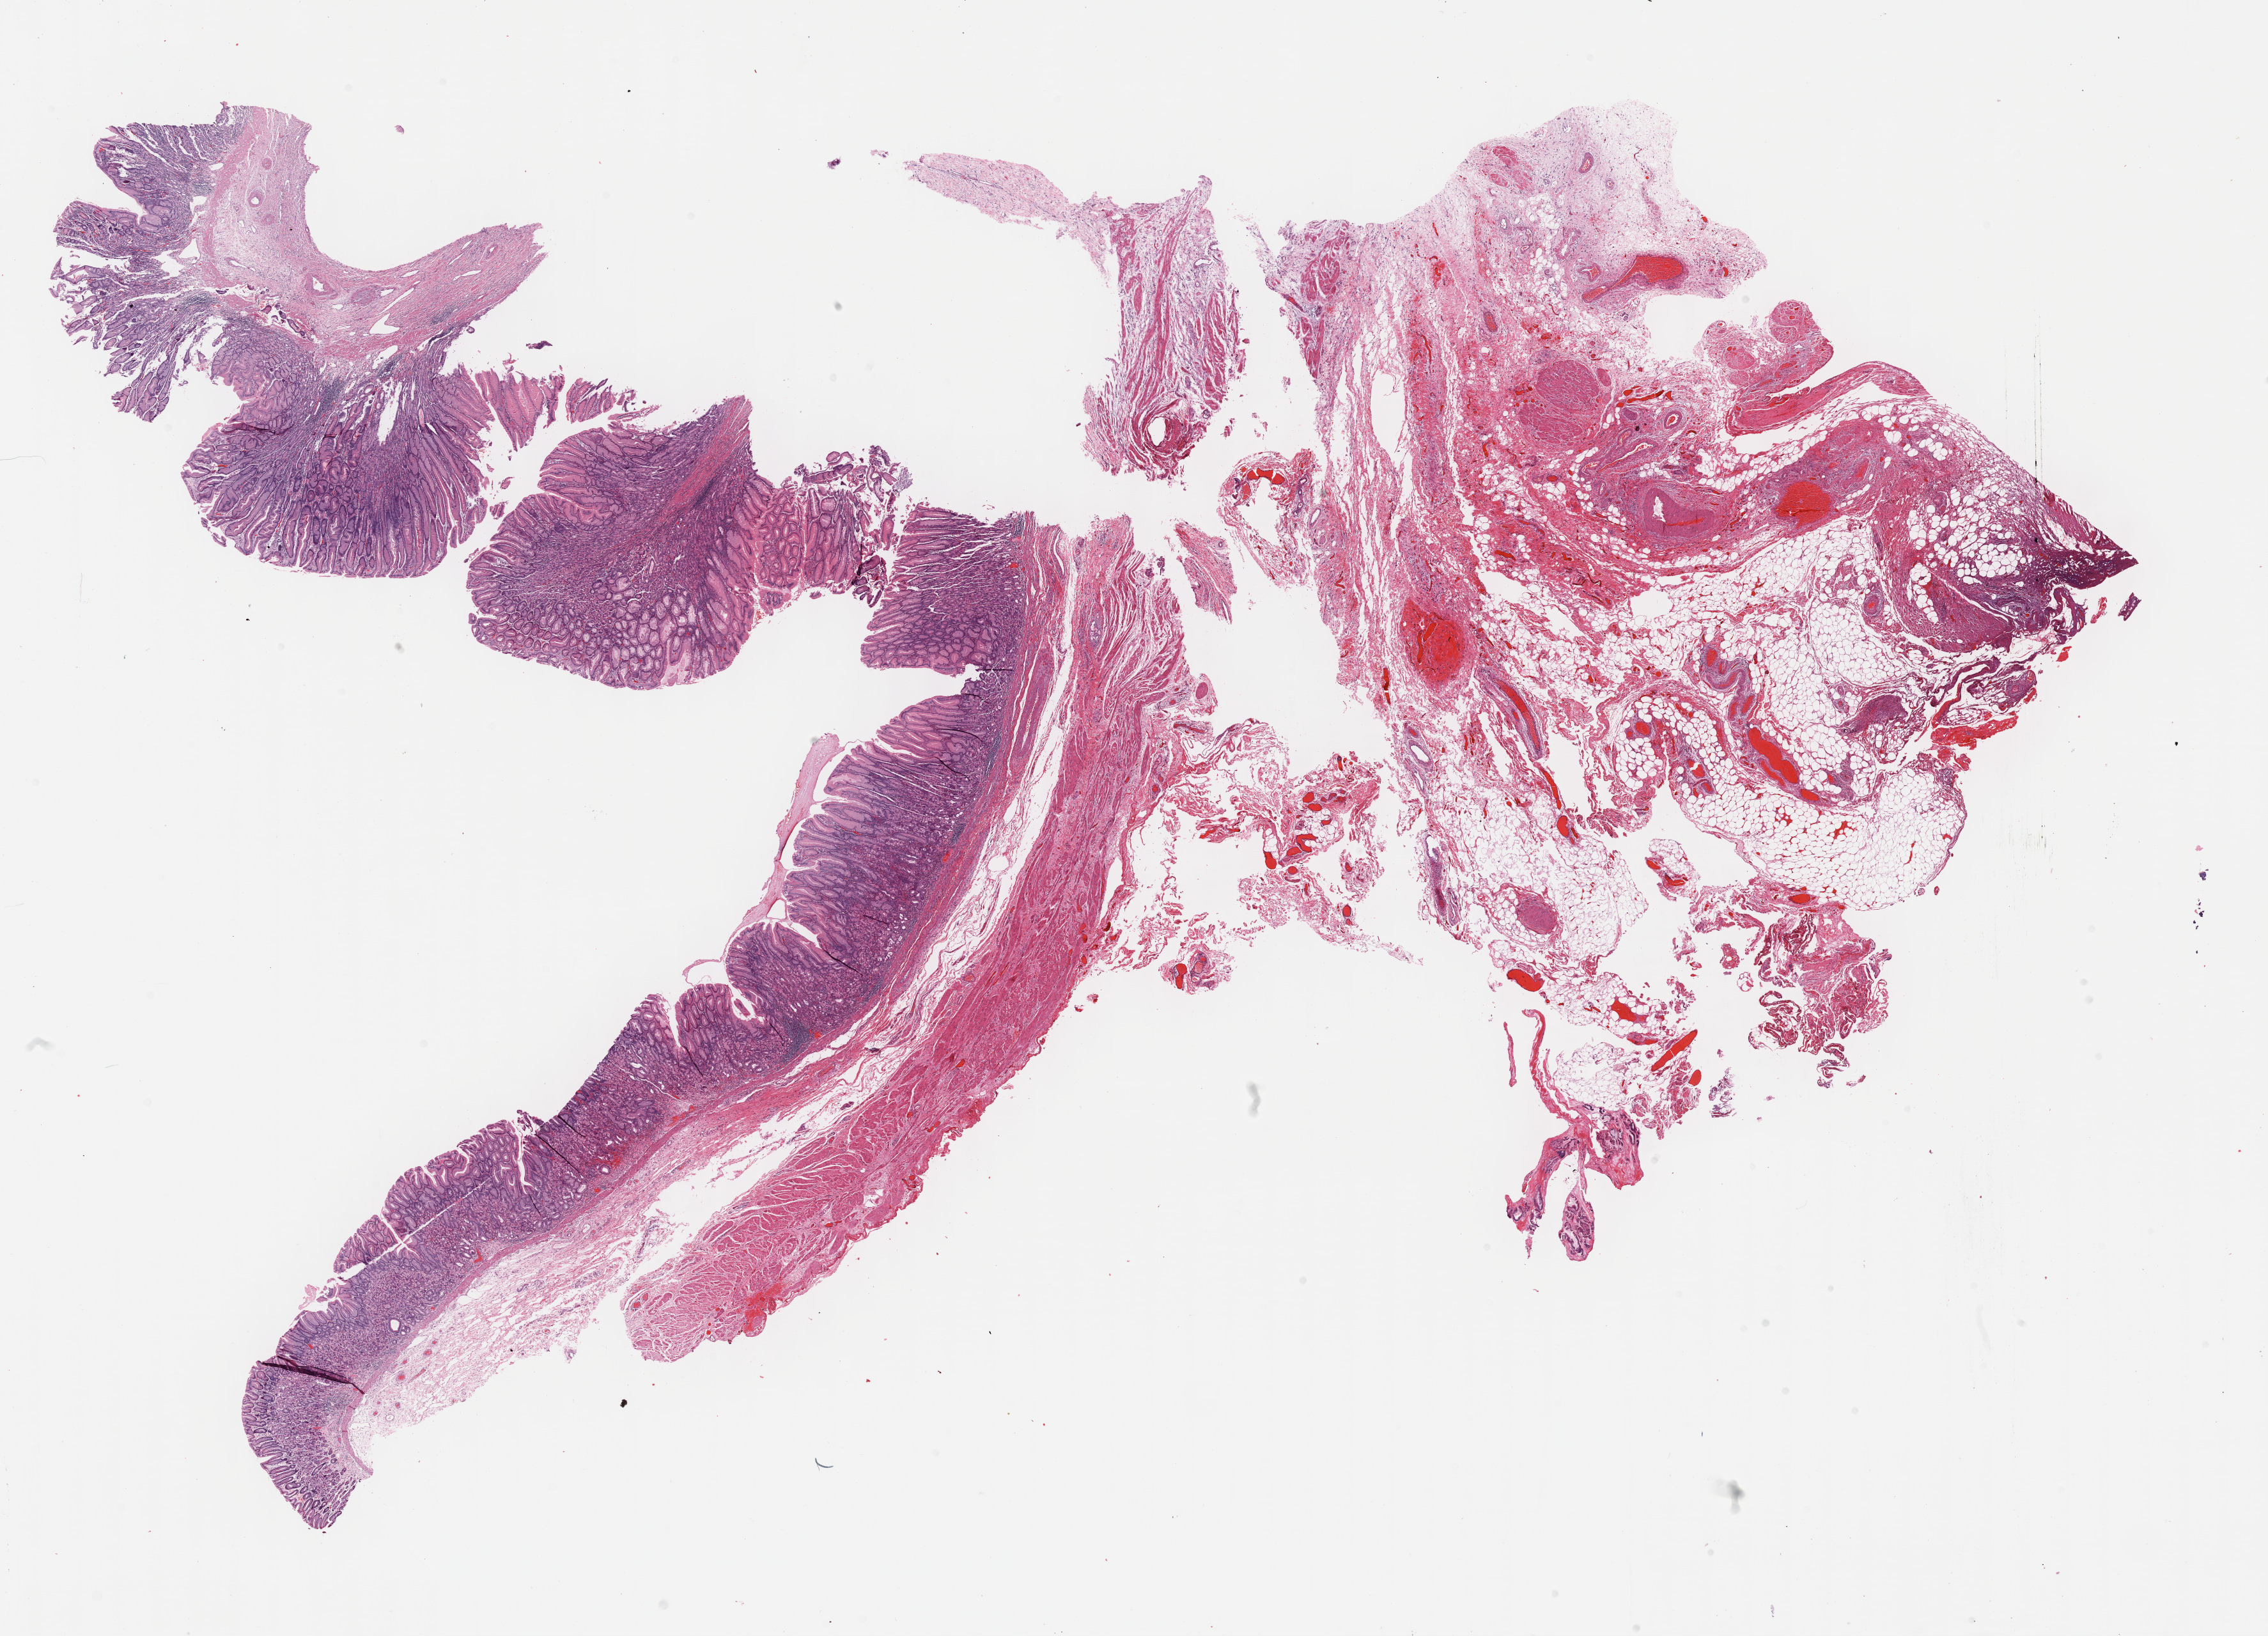
Hematoxylin and eosin (H&E) stained whole-slide image, shown as a low-resolution overview of the whole scanned area (about 28.7 x 20.7 mm); FFPE section; sample: primary tumour, stomach. Female patient; age at initial diagnosis 58 years.
• histologic diagnosis: Leiomyosarcoma, NOS